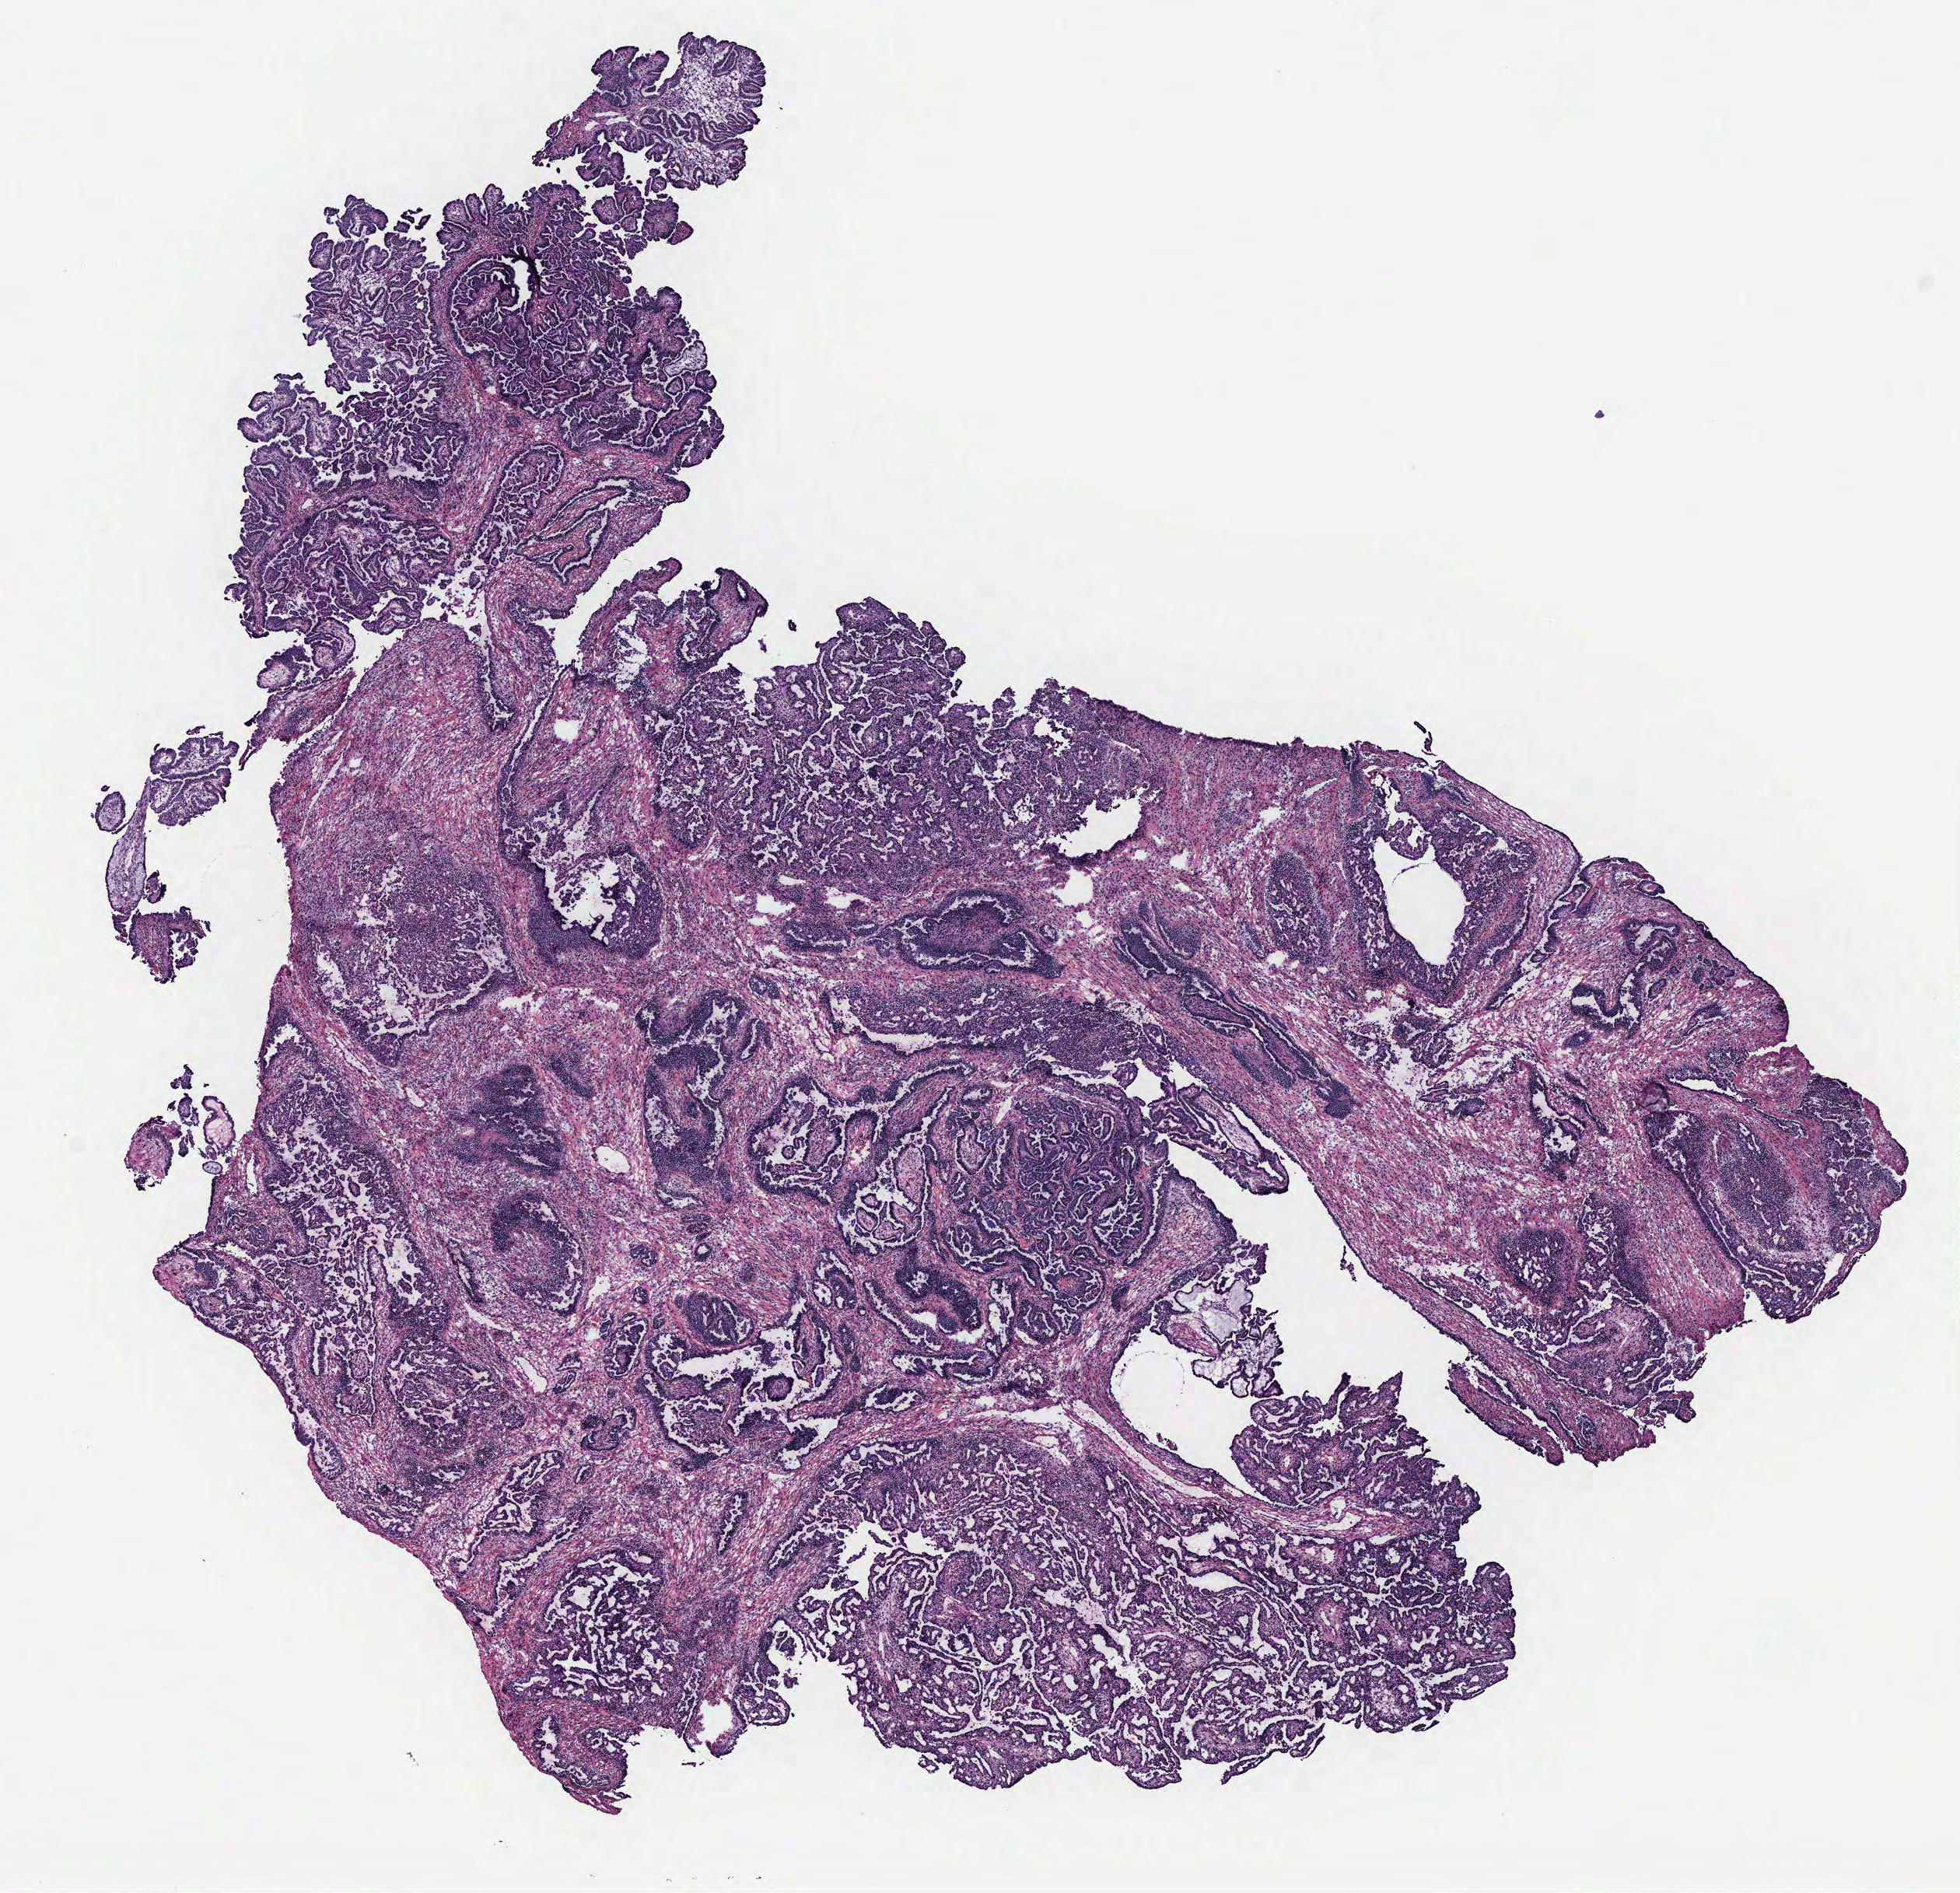
Hematoxylin and eosin (H&E) stained whole-slide image — low-resolution overview of the scanned area, about 10.1 x 9.7 mm. Ovary, tumour tissue. 46-year-old female patient.
Diagnosis: Serous adenocarcinoma, NOS. Primary tumour site (as recorded): ovary.